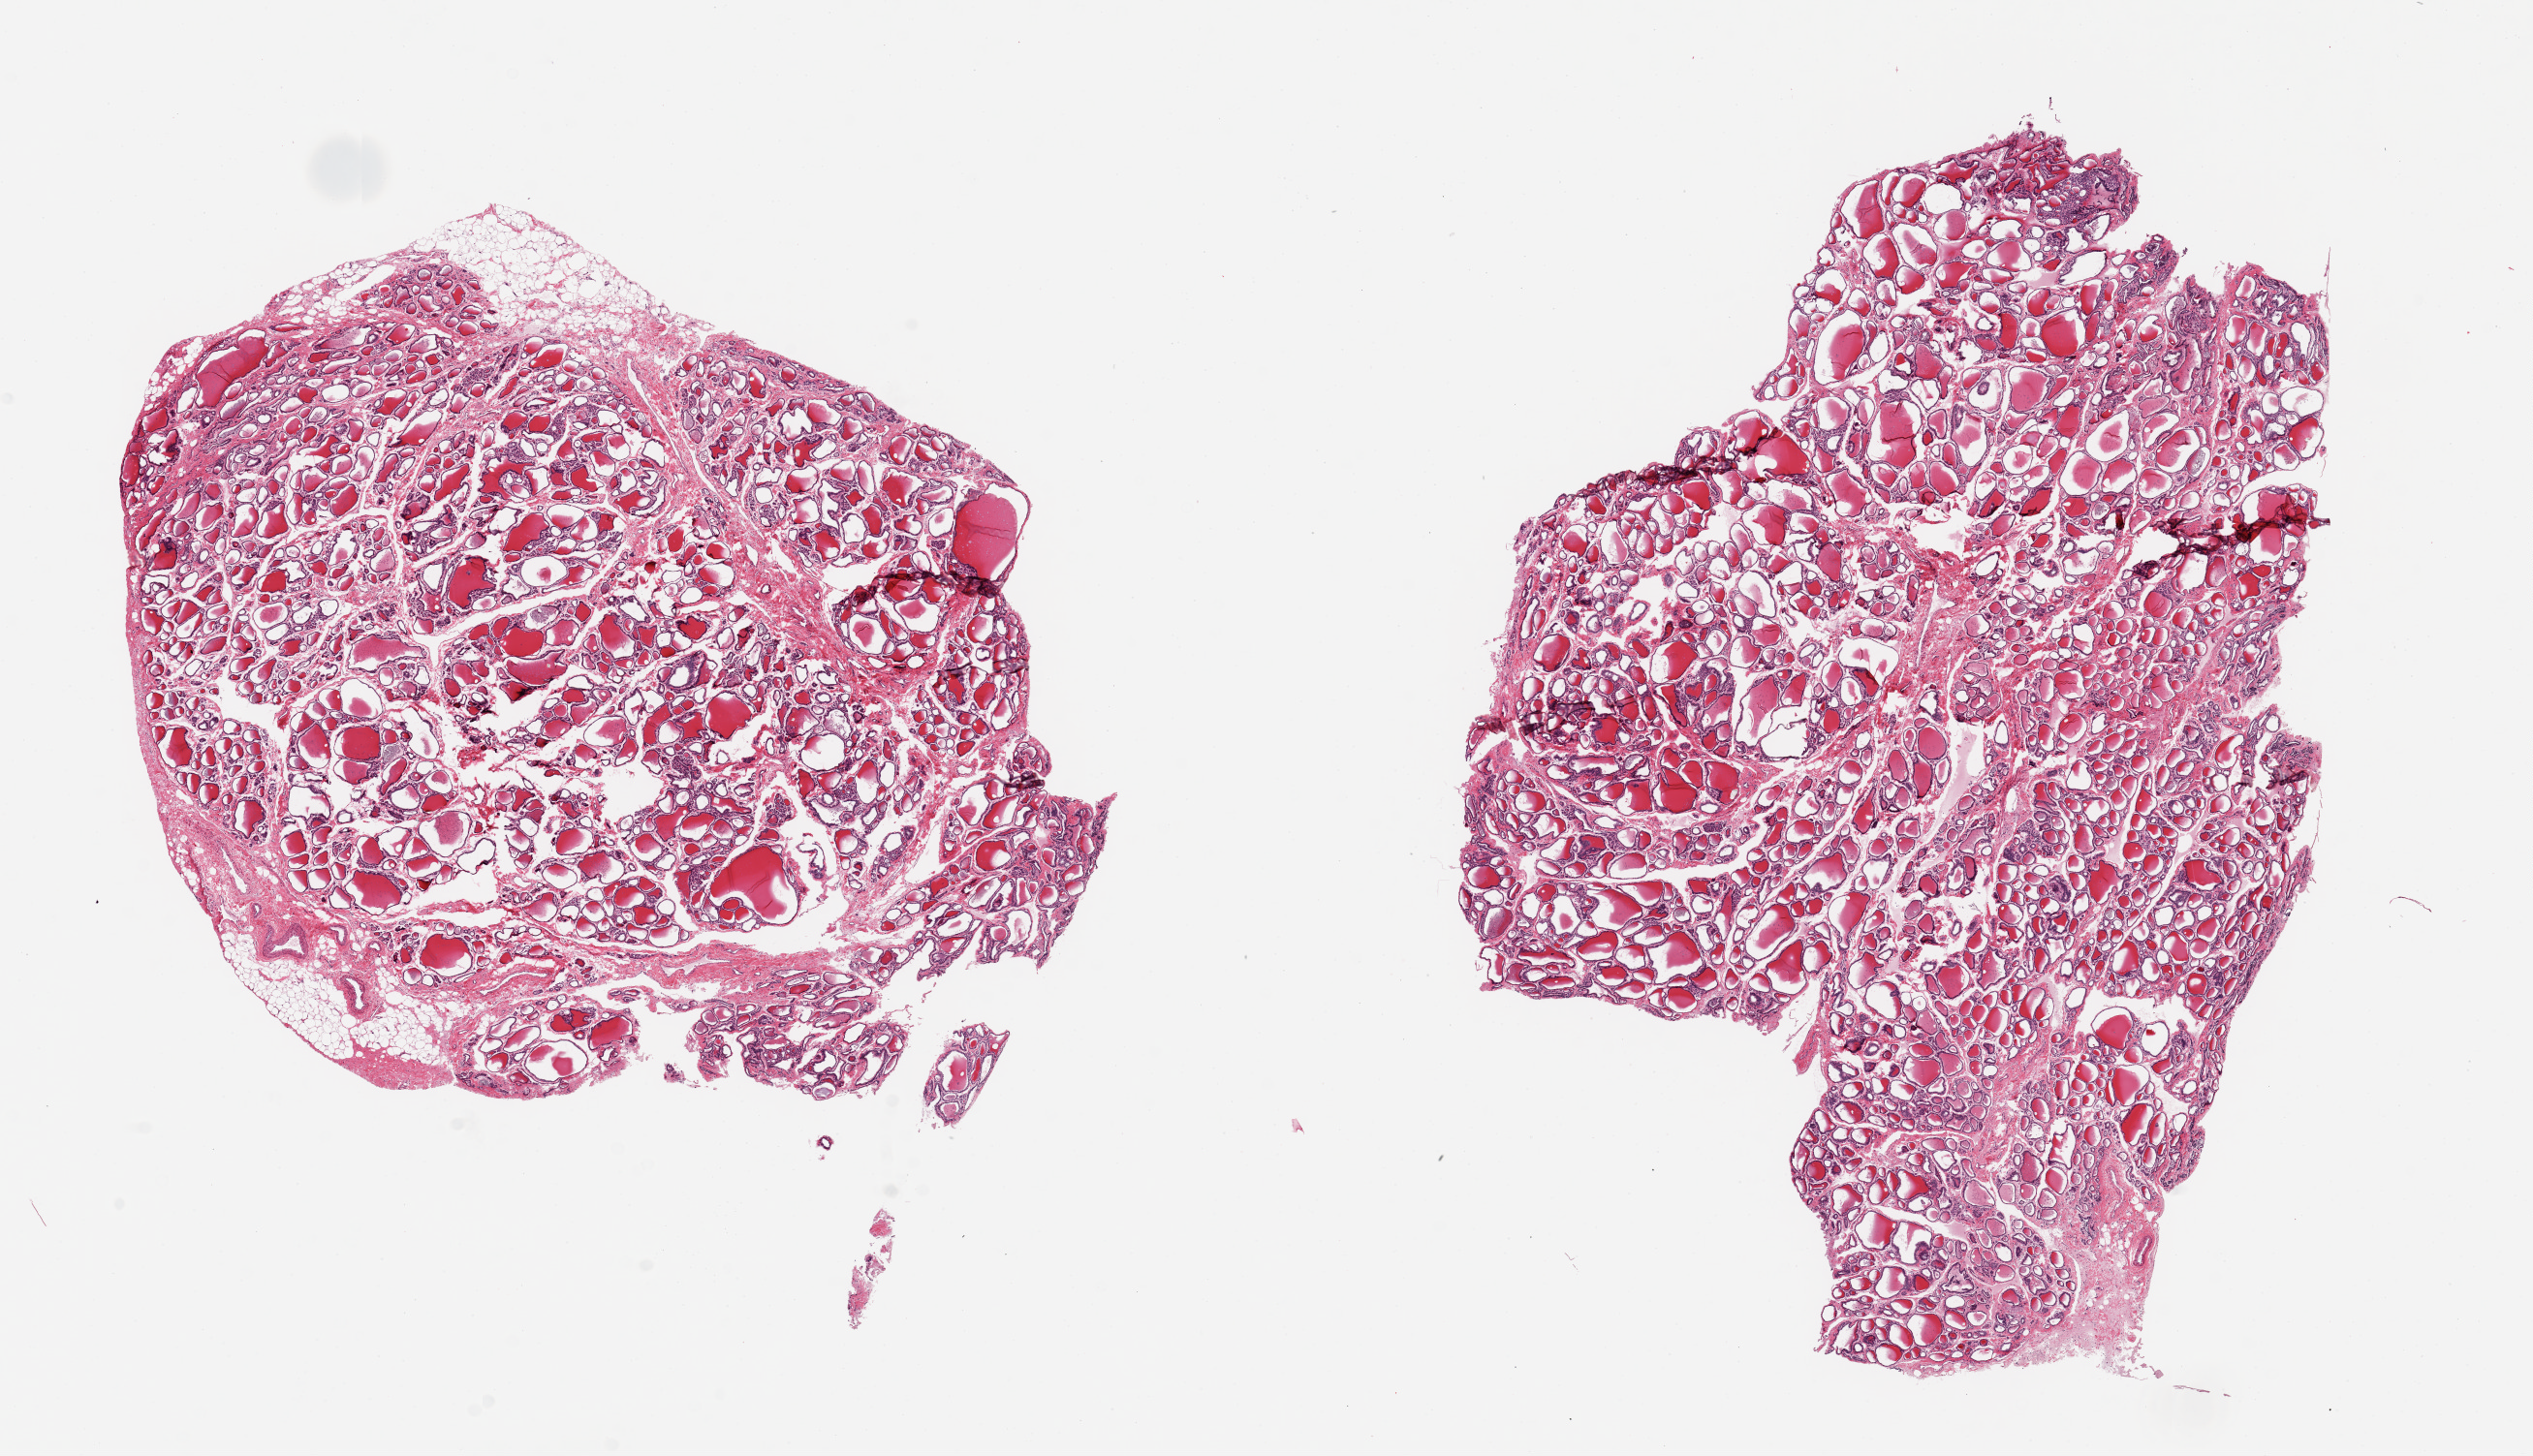
Whole-slide image, haematoxylin and eosin stain — low-resolution overview of the scanned area, about 20.7 x 11.9 mm (acquisition: 20x scan). PAXgene-fixed paraffin-embedded (PFPE) section. Sampled site (target tissue): thyroid. Donor tissue sample. Male donor.
Review note (as recorded): 2pieces ~8x7mm. Regressive/fibrotic features.